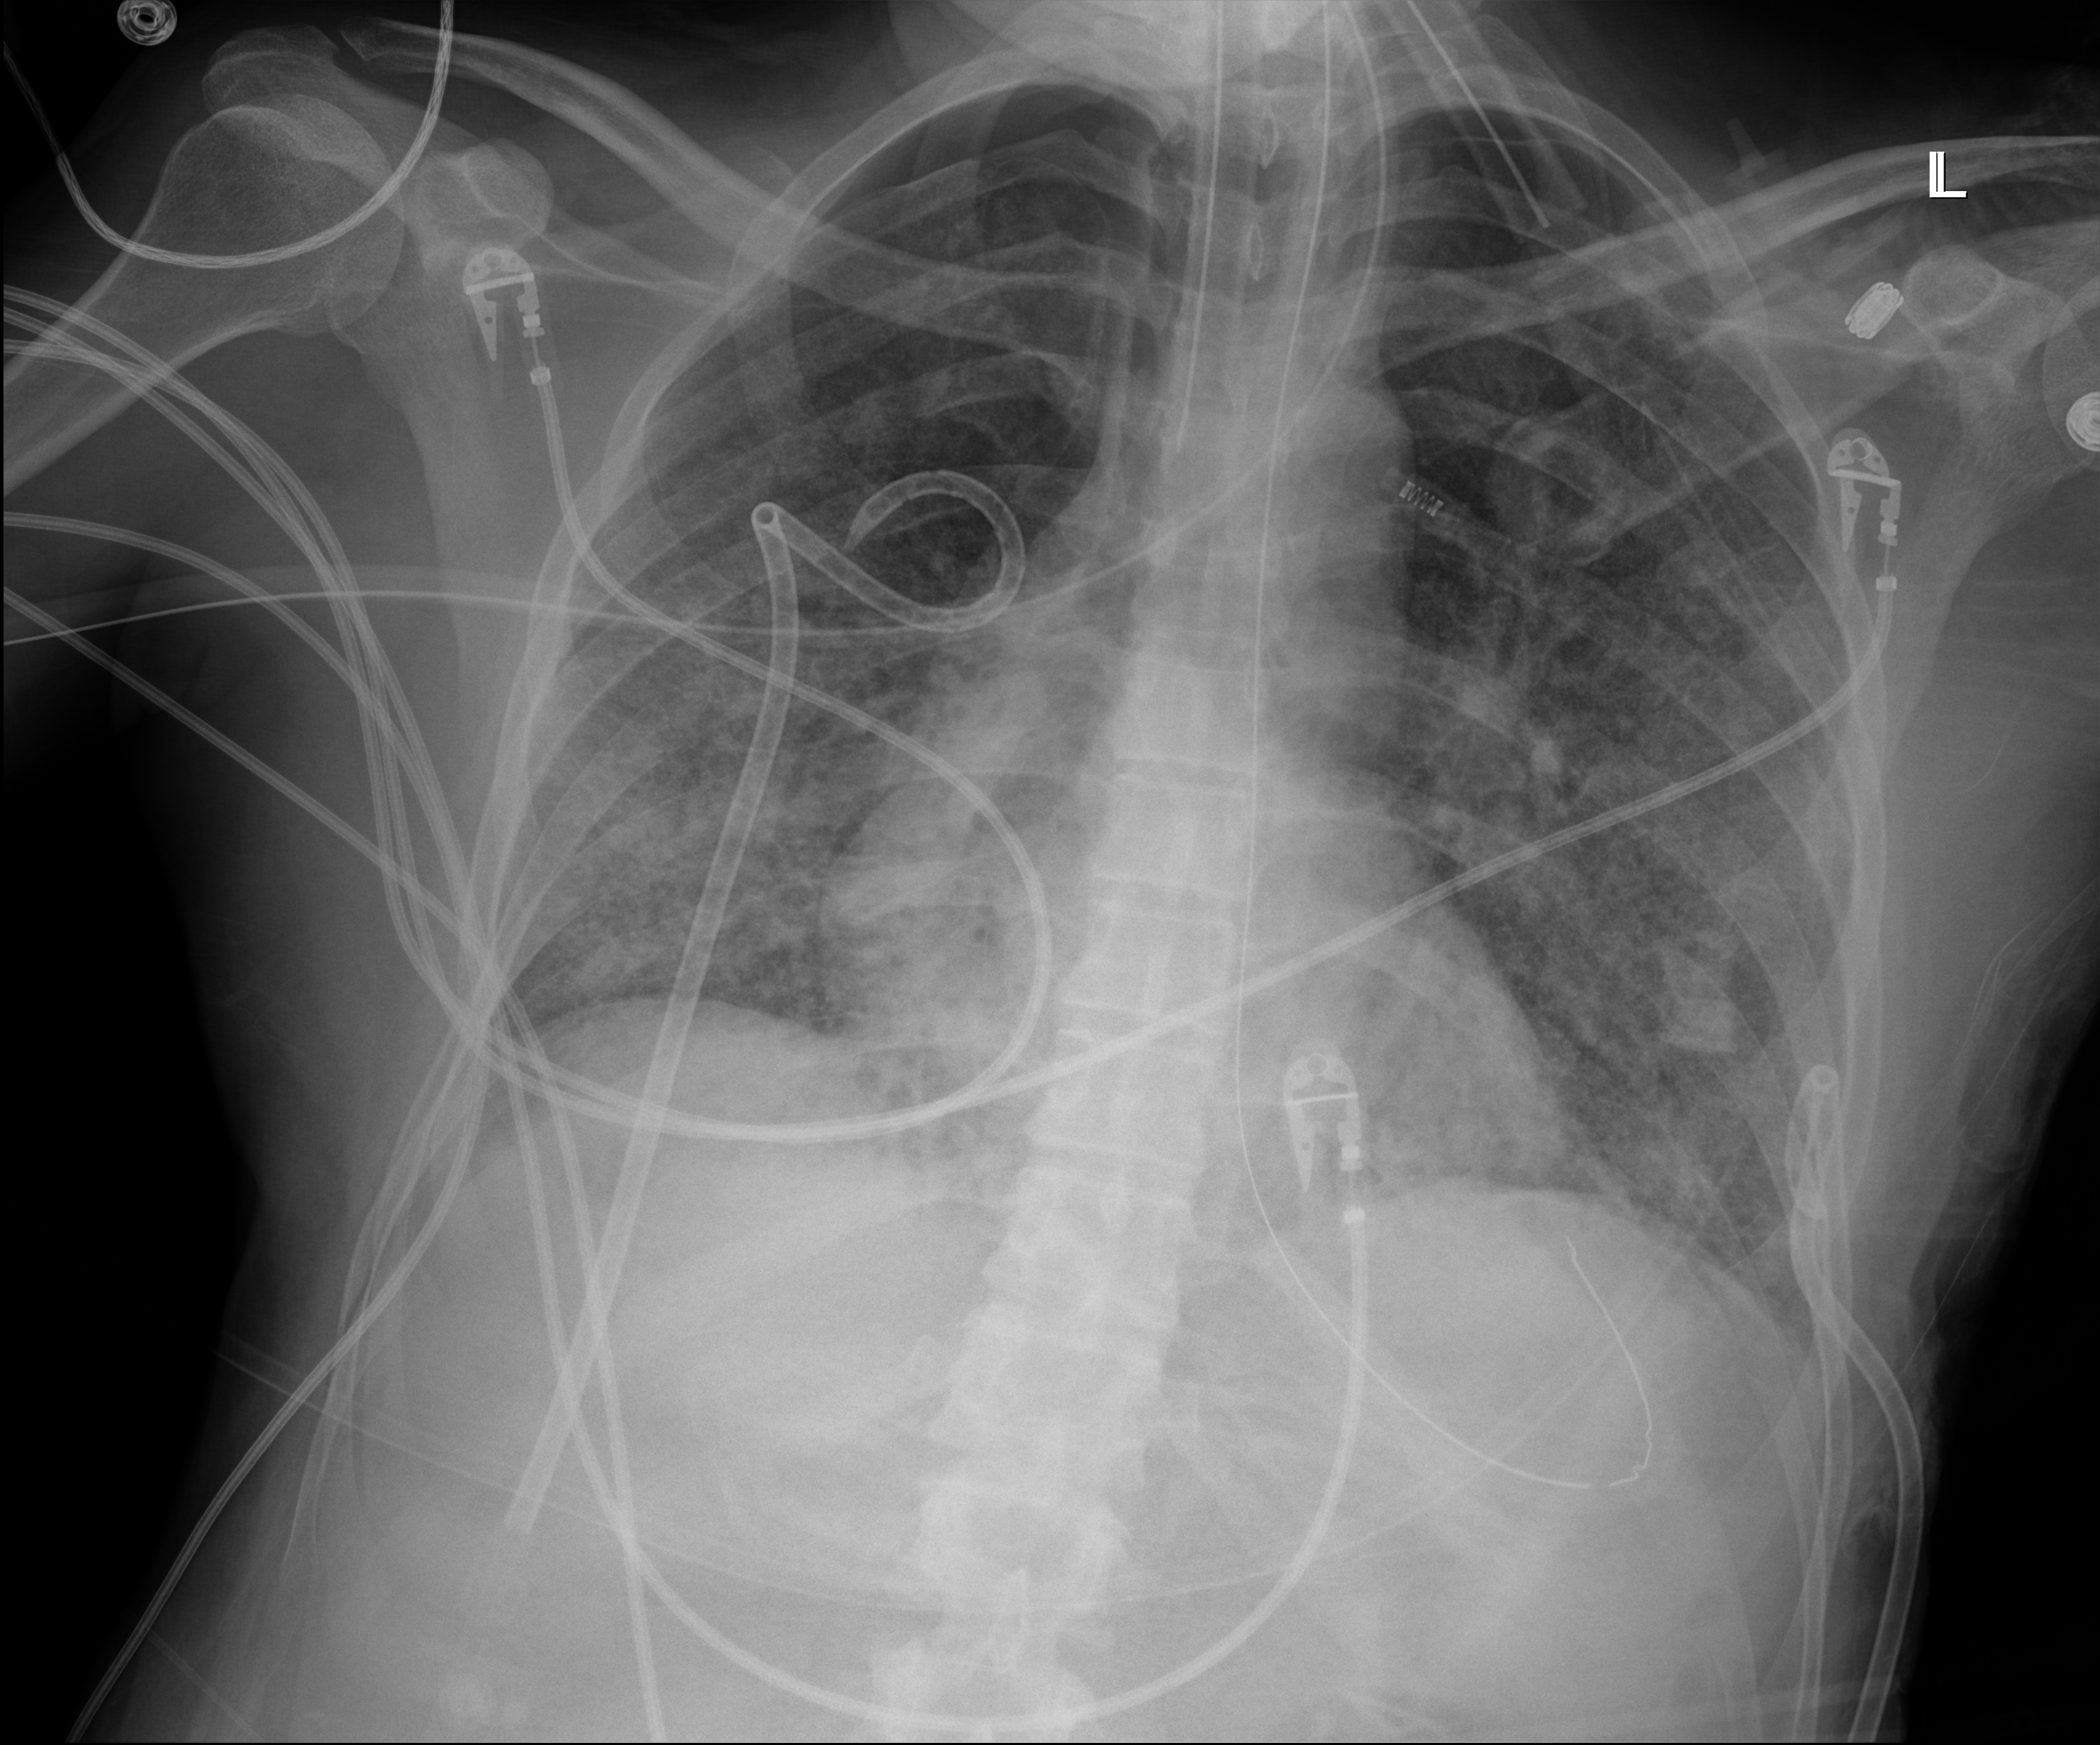
Bedside chest radiograph (digital radiography); anteroposterior (AP) projection. Patient hospitalised with COVID-19, aged 18–59 years.
Admission-level facts for this patient (not findings on this image; timing relative to this image not recorded):
- hypertension (admission record): no